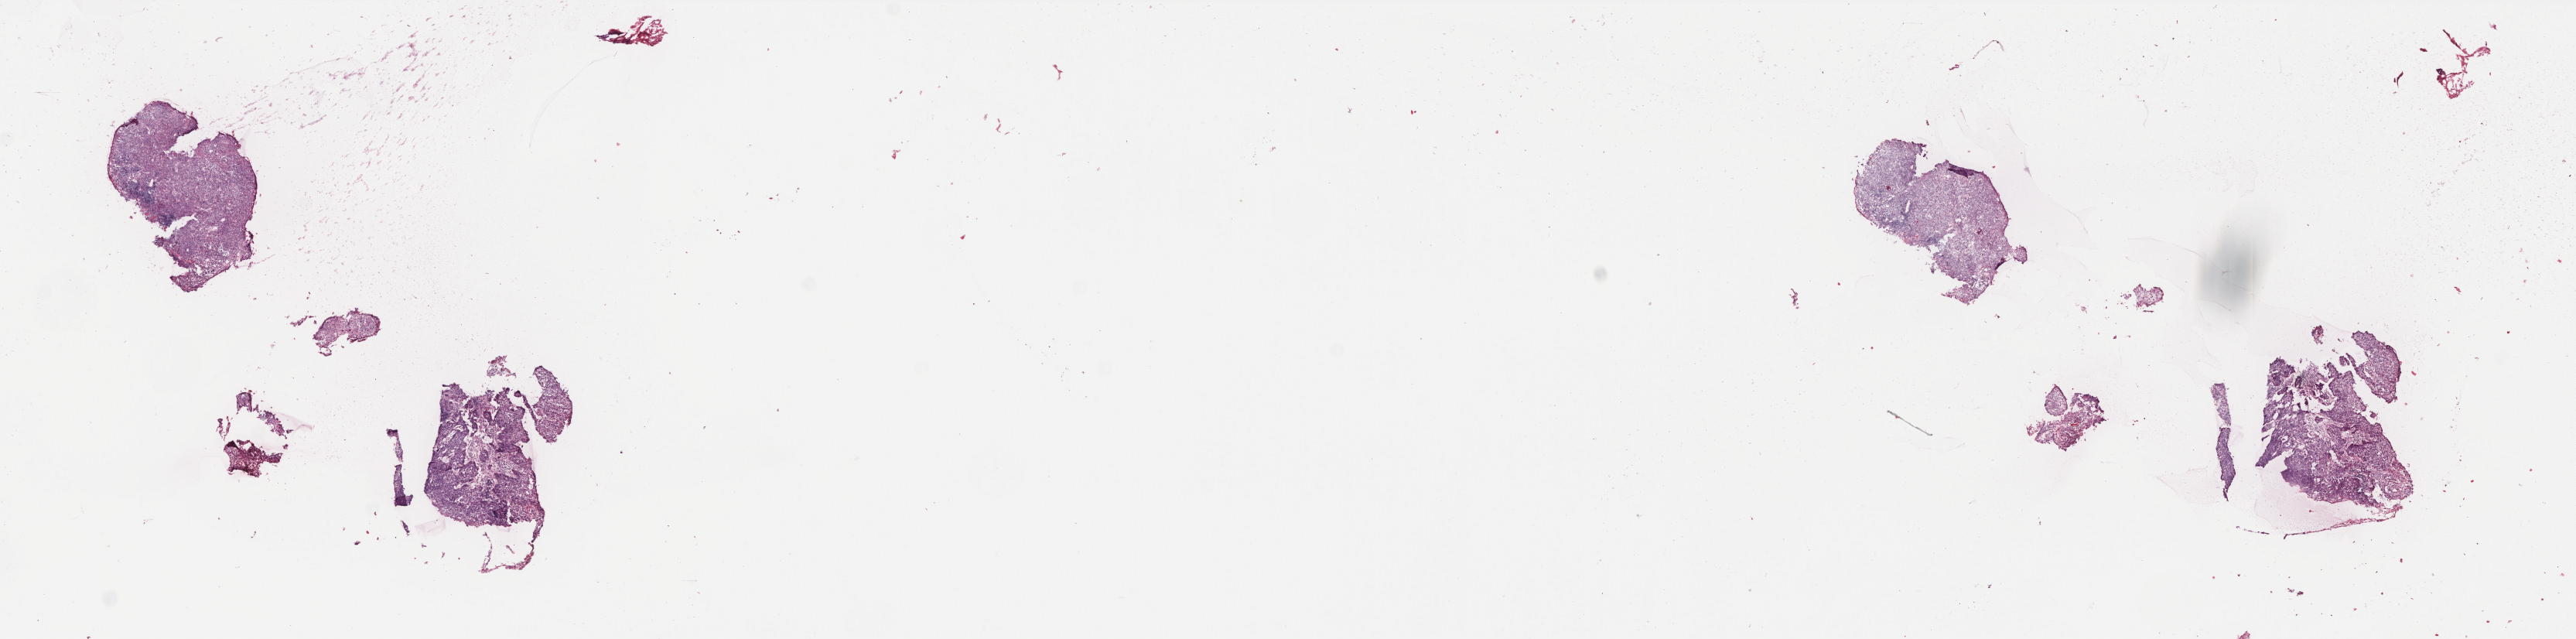
Whole-slide histology image, Hematoxylin and eosin (H&E) stained, low-resolution overview of the scanned area, about 26.7 x 6.6 mm; frozen section from the top of the tissue portion; sample: primary tumour, cervix. Patient: female, age at initial diagnosis 21 years.
Pathologic diagnosis: Squamous cell carcinoma, keratinizing, NOS (cervix uteri).